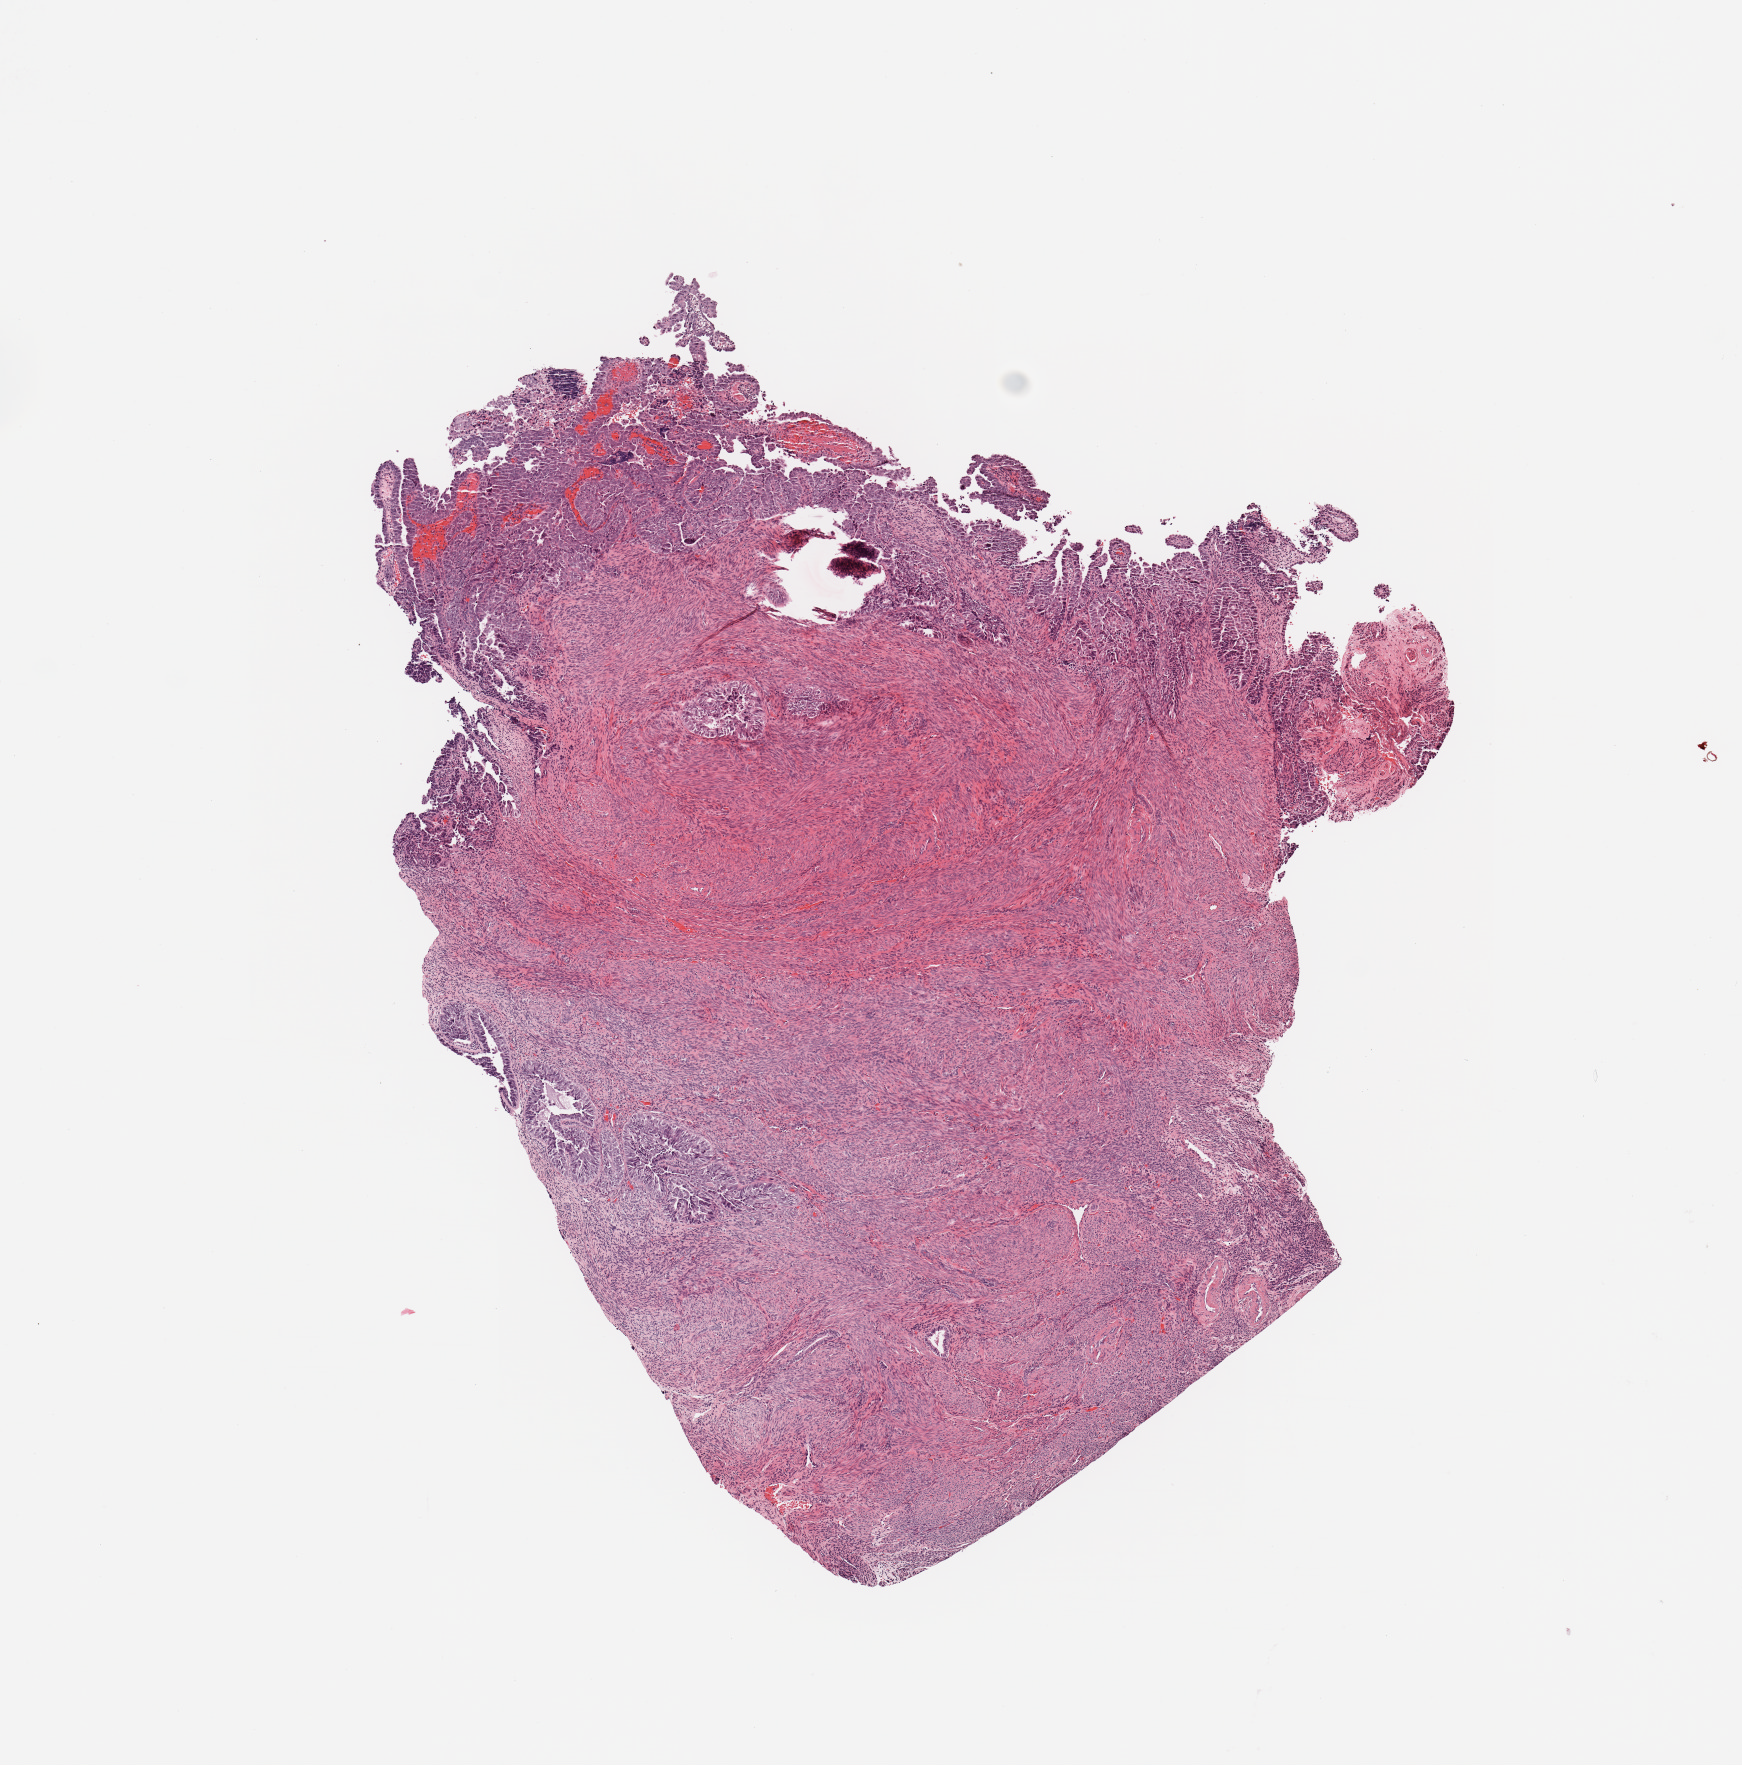
Whole-slide histology image, H&E, a low-resolution overview of the entire scanned area, about 6.9 x 7.0 mm. Uterus, tumour tissue. 70-year-old female patient.
Patient diagnosis (cohort enrolment): corpus endometrial carcinoma (uterus).